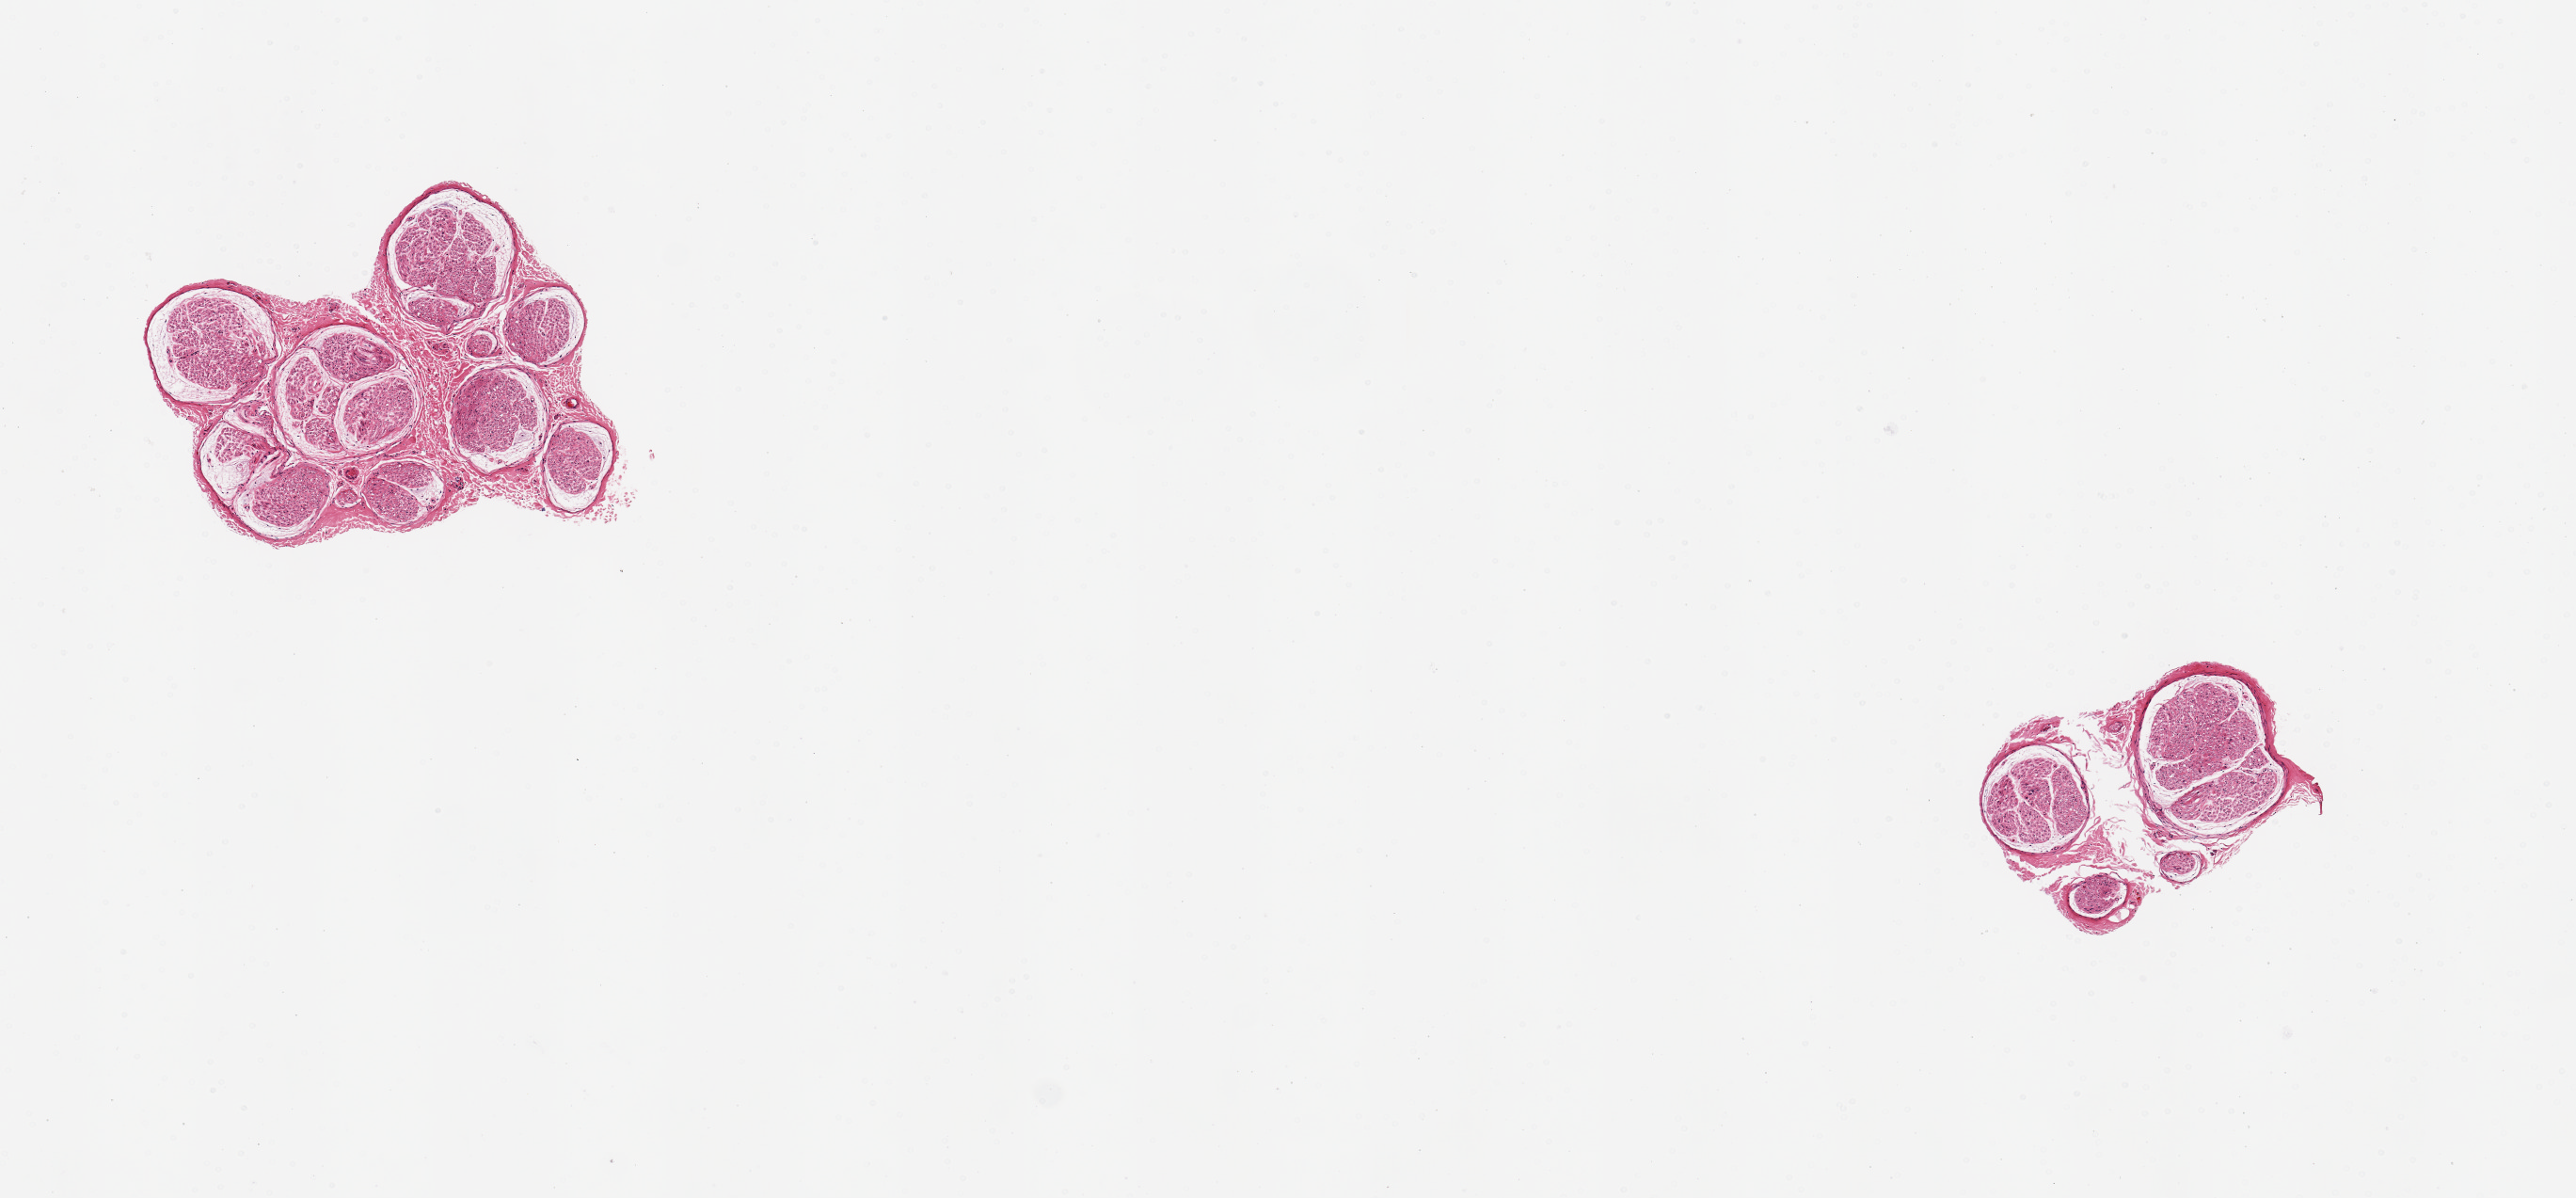
Hematoxylin and eosin (H&E) whole-slide image, shown as a low-resolution overview of the whole scanned area (about 10.8 x 5.0 mm). PAXgene-fixed, paraffin-embedded tissue. Section of tibial nerve (target tissue). Tissue donor sample. Donor: female.
Pathologist's review note for this sample: 2 aliquots, ~2mm d peripheral nerve, no artery present. May be retained for study as nerve after re-labeling.